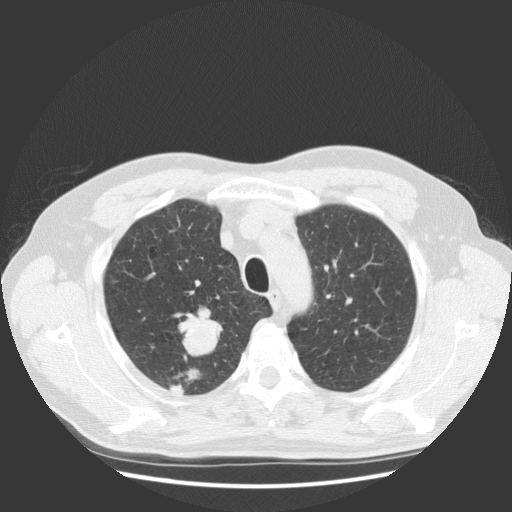
Low-dose screening chest CT, one axial slice; position 101 of 131 along the scan axis; reconstruction kernel STANDARD; 140 kVp; lung window (W 1500 / L -600 HU); 512 × 512 image matrix, field of view 369 × 369 mm.
Outlined on this slice (expert manual segmentation):
- lesion 1 (tumor, upper lobe of right lung): bounding box <178,307,222,356> (left, top, right, bottom; pixels)
- lesion 2 (tumor, upper lobe of right lung): <170,369,200,394>